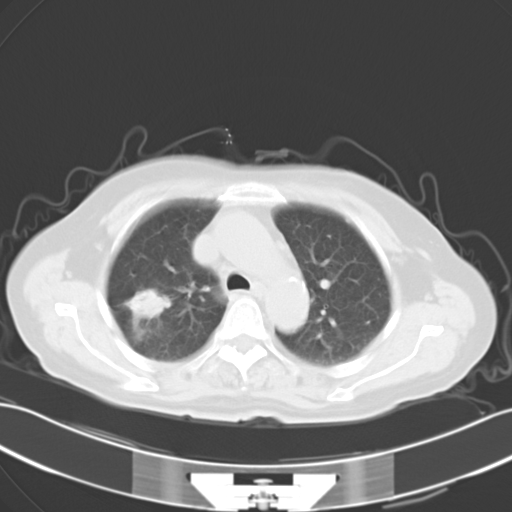
Chest CT, one axial slice. Position 21 of 28 along the scan axis. Reconstruction kernel B40f. Lung window (W 1500 / L -600 HU). 512 × 512 image matrix, field of view 353 × 353 mm. Patient: female, 65 years. From the clinical record (not read from this slice): clinical TNM (as recorded): T1c N0 M1c.
Annotated regions visible in this slice (rectangle marked by the reading radiologist):
- lung tumour (recorded histology: adenocarcinoma): bounding box [x1, y1, x2, y2] px = [130, 286, 172, 319]